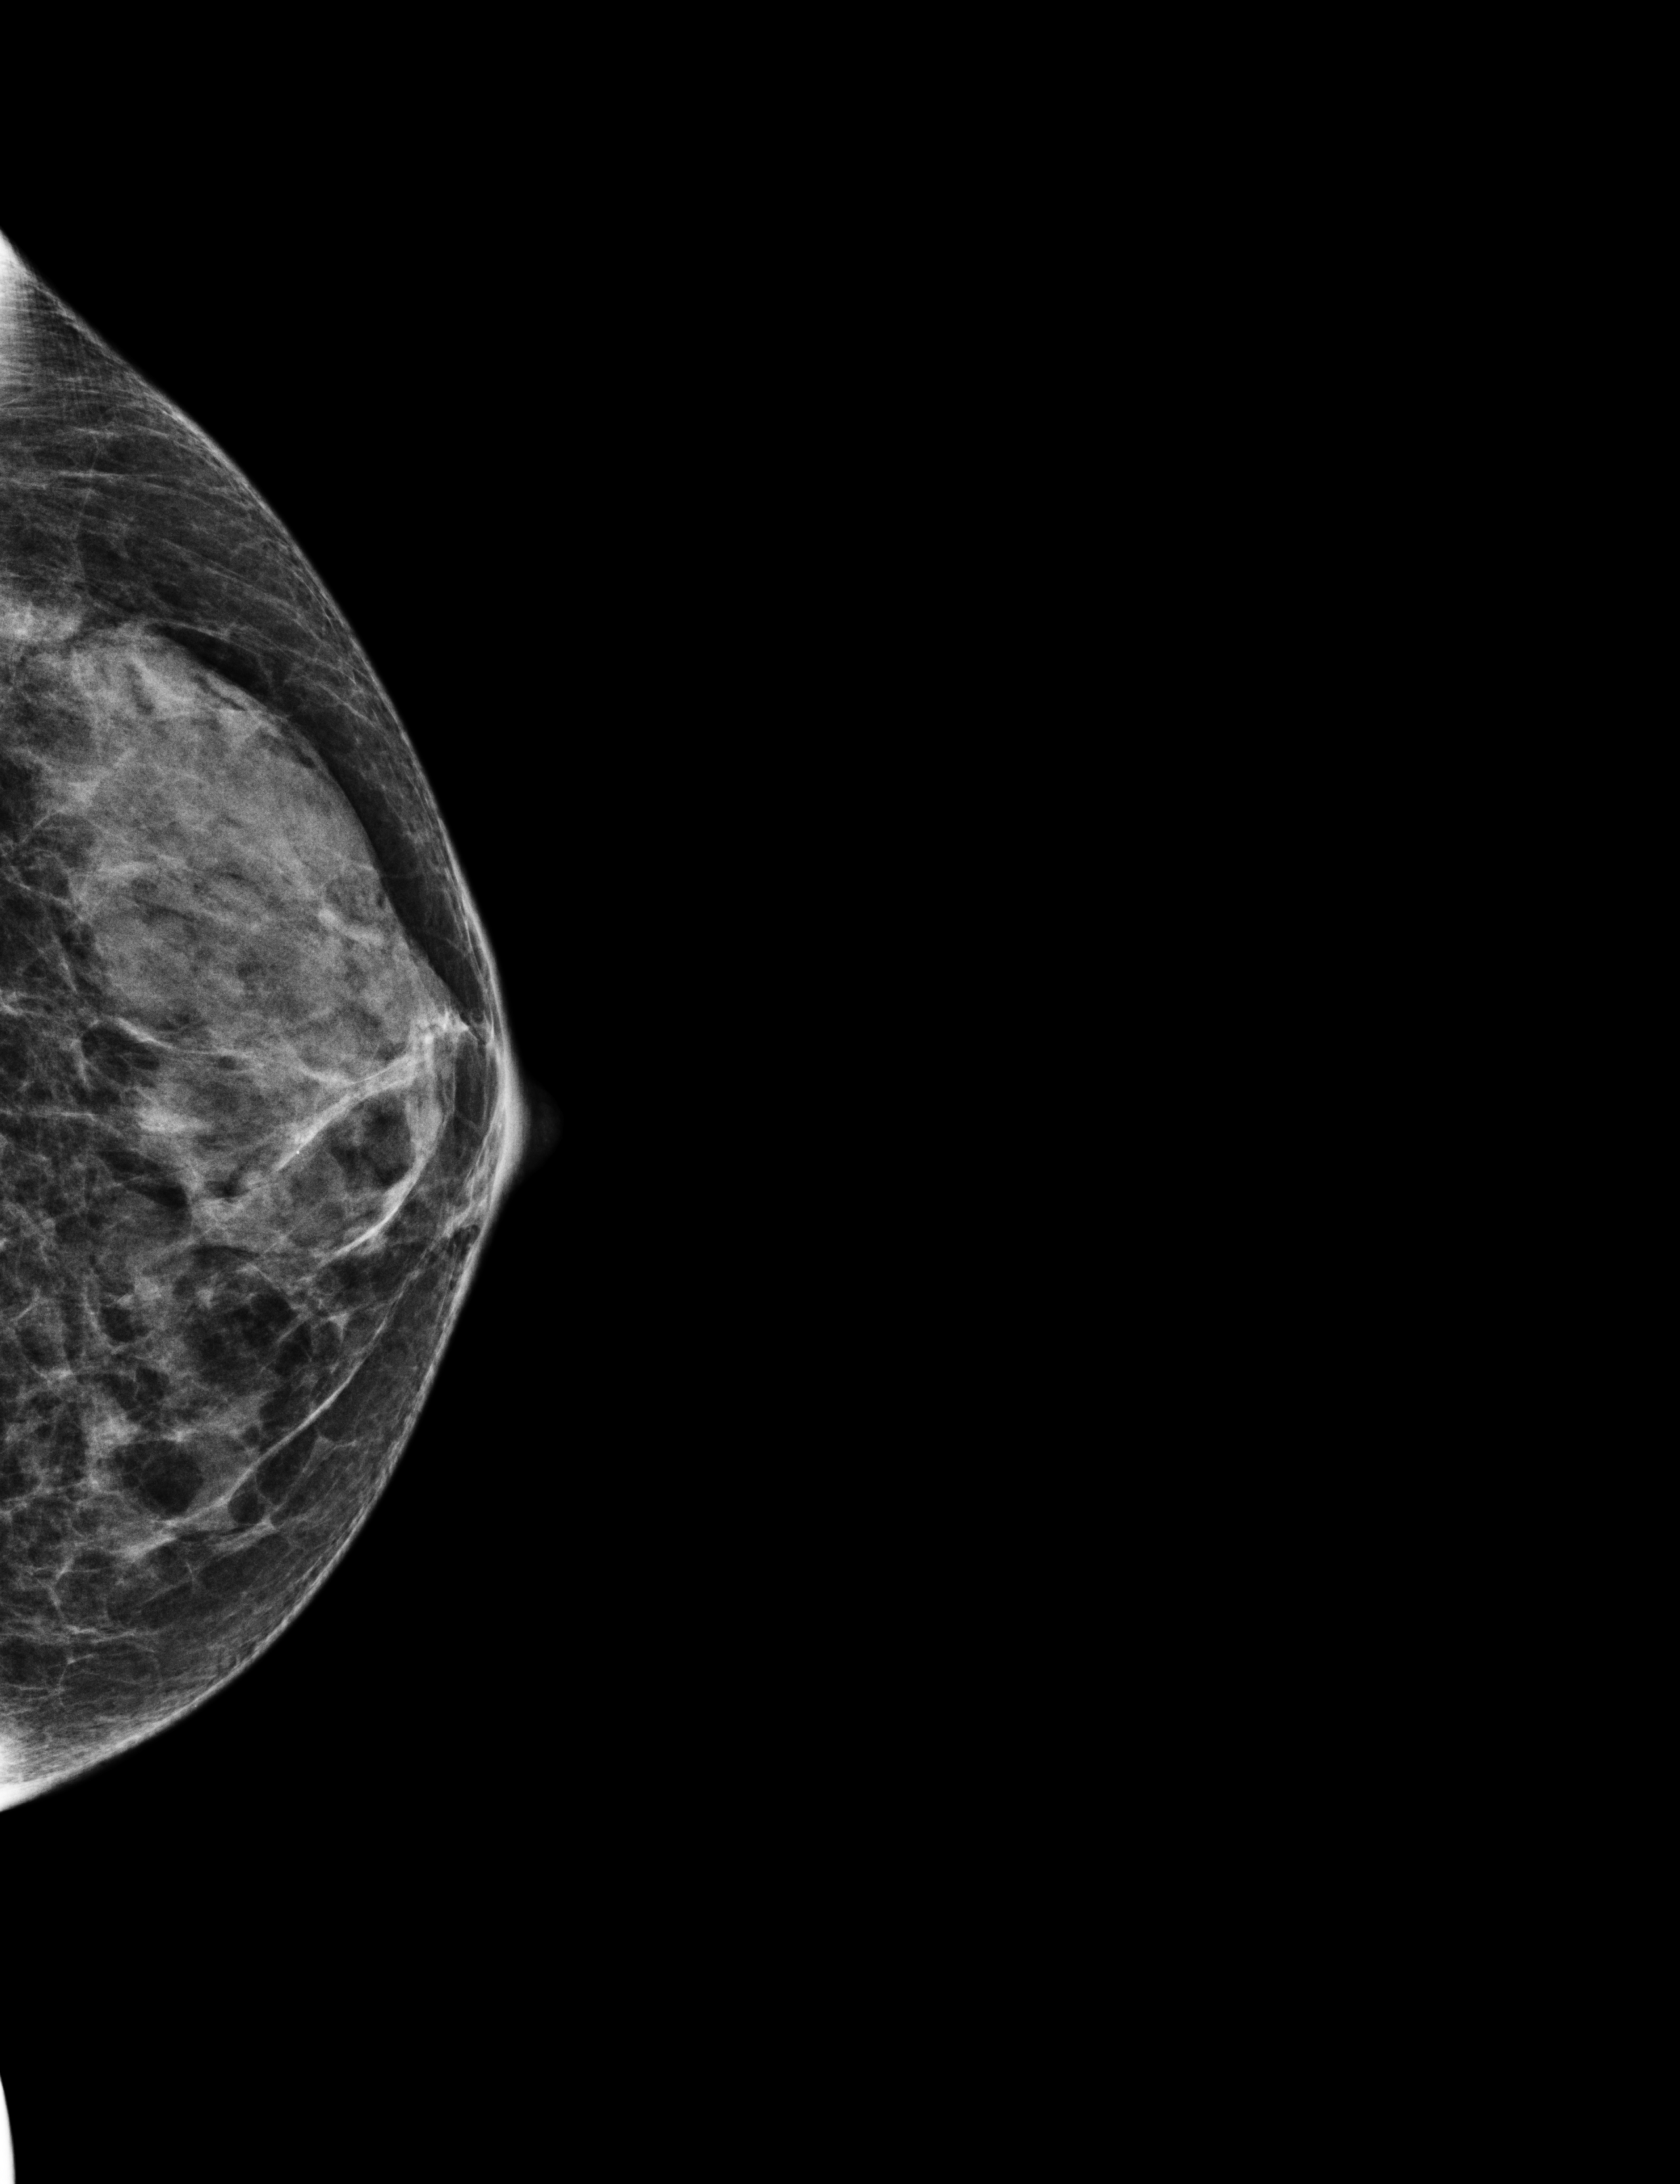
Screening examination, system: Selenia Dimensions. Female patient, age 61 years.
Image type: full-field digital mammogram. Breast: left. Projection: cranio-caudal projection.